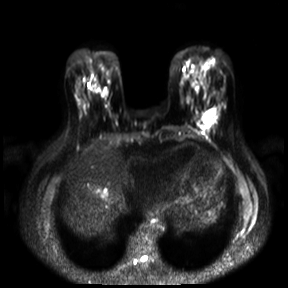
Breast MRI, one axial slice; position 8 of 30 along the scan axis; diffusion-weighted series; image 2 of 4 stored at this slice position (different b-values; order by instance number); 3 T; 288 × 288 image matrix, field of view 360 × 360 mm. Female patient.
Structures marked on this image (outlined manually by an expert reader):
- tumour on diffusion-weighted imaging: bounding box <203,110,214,124> (left, top, right, bottom; pixels)